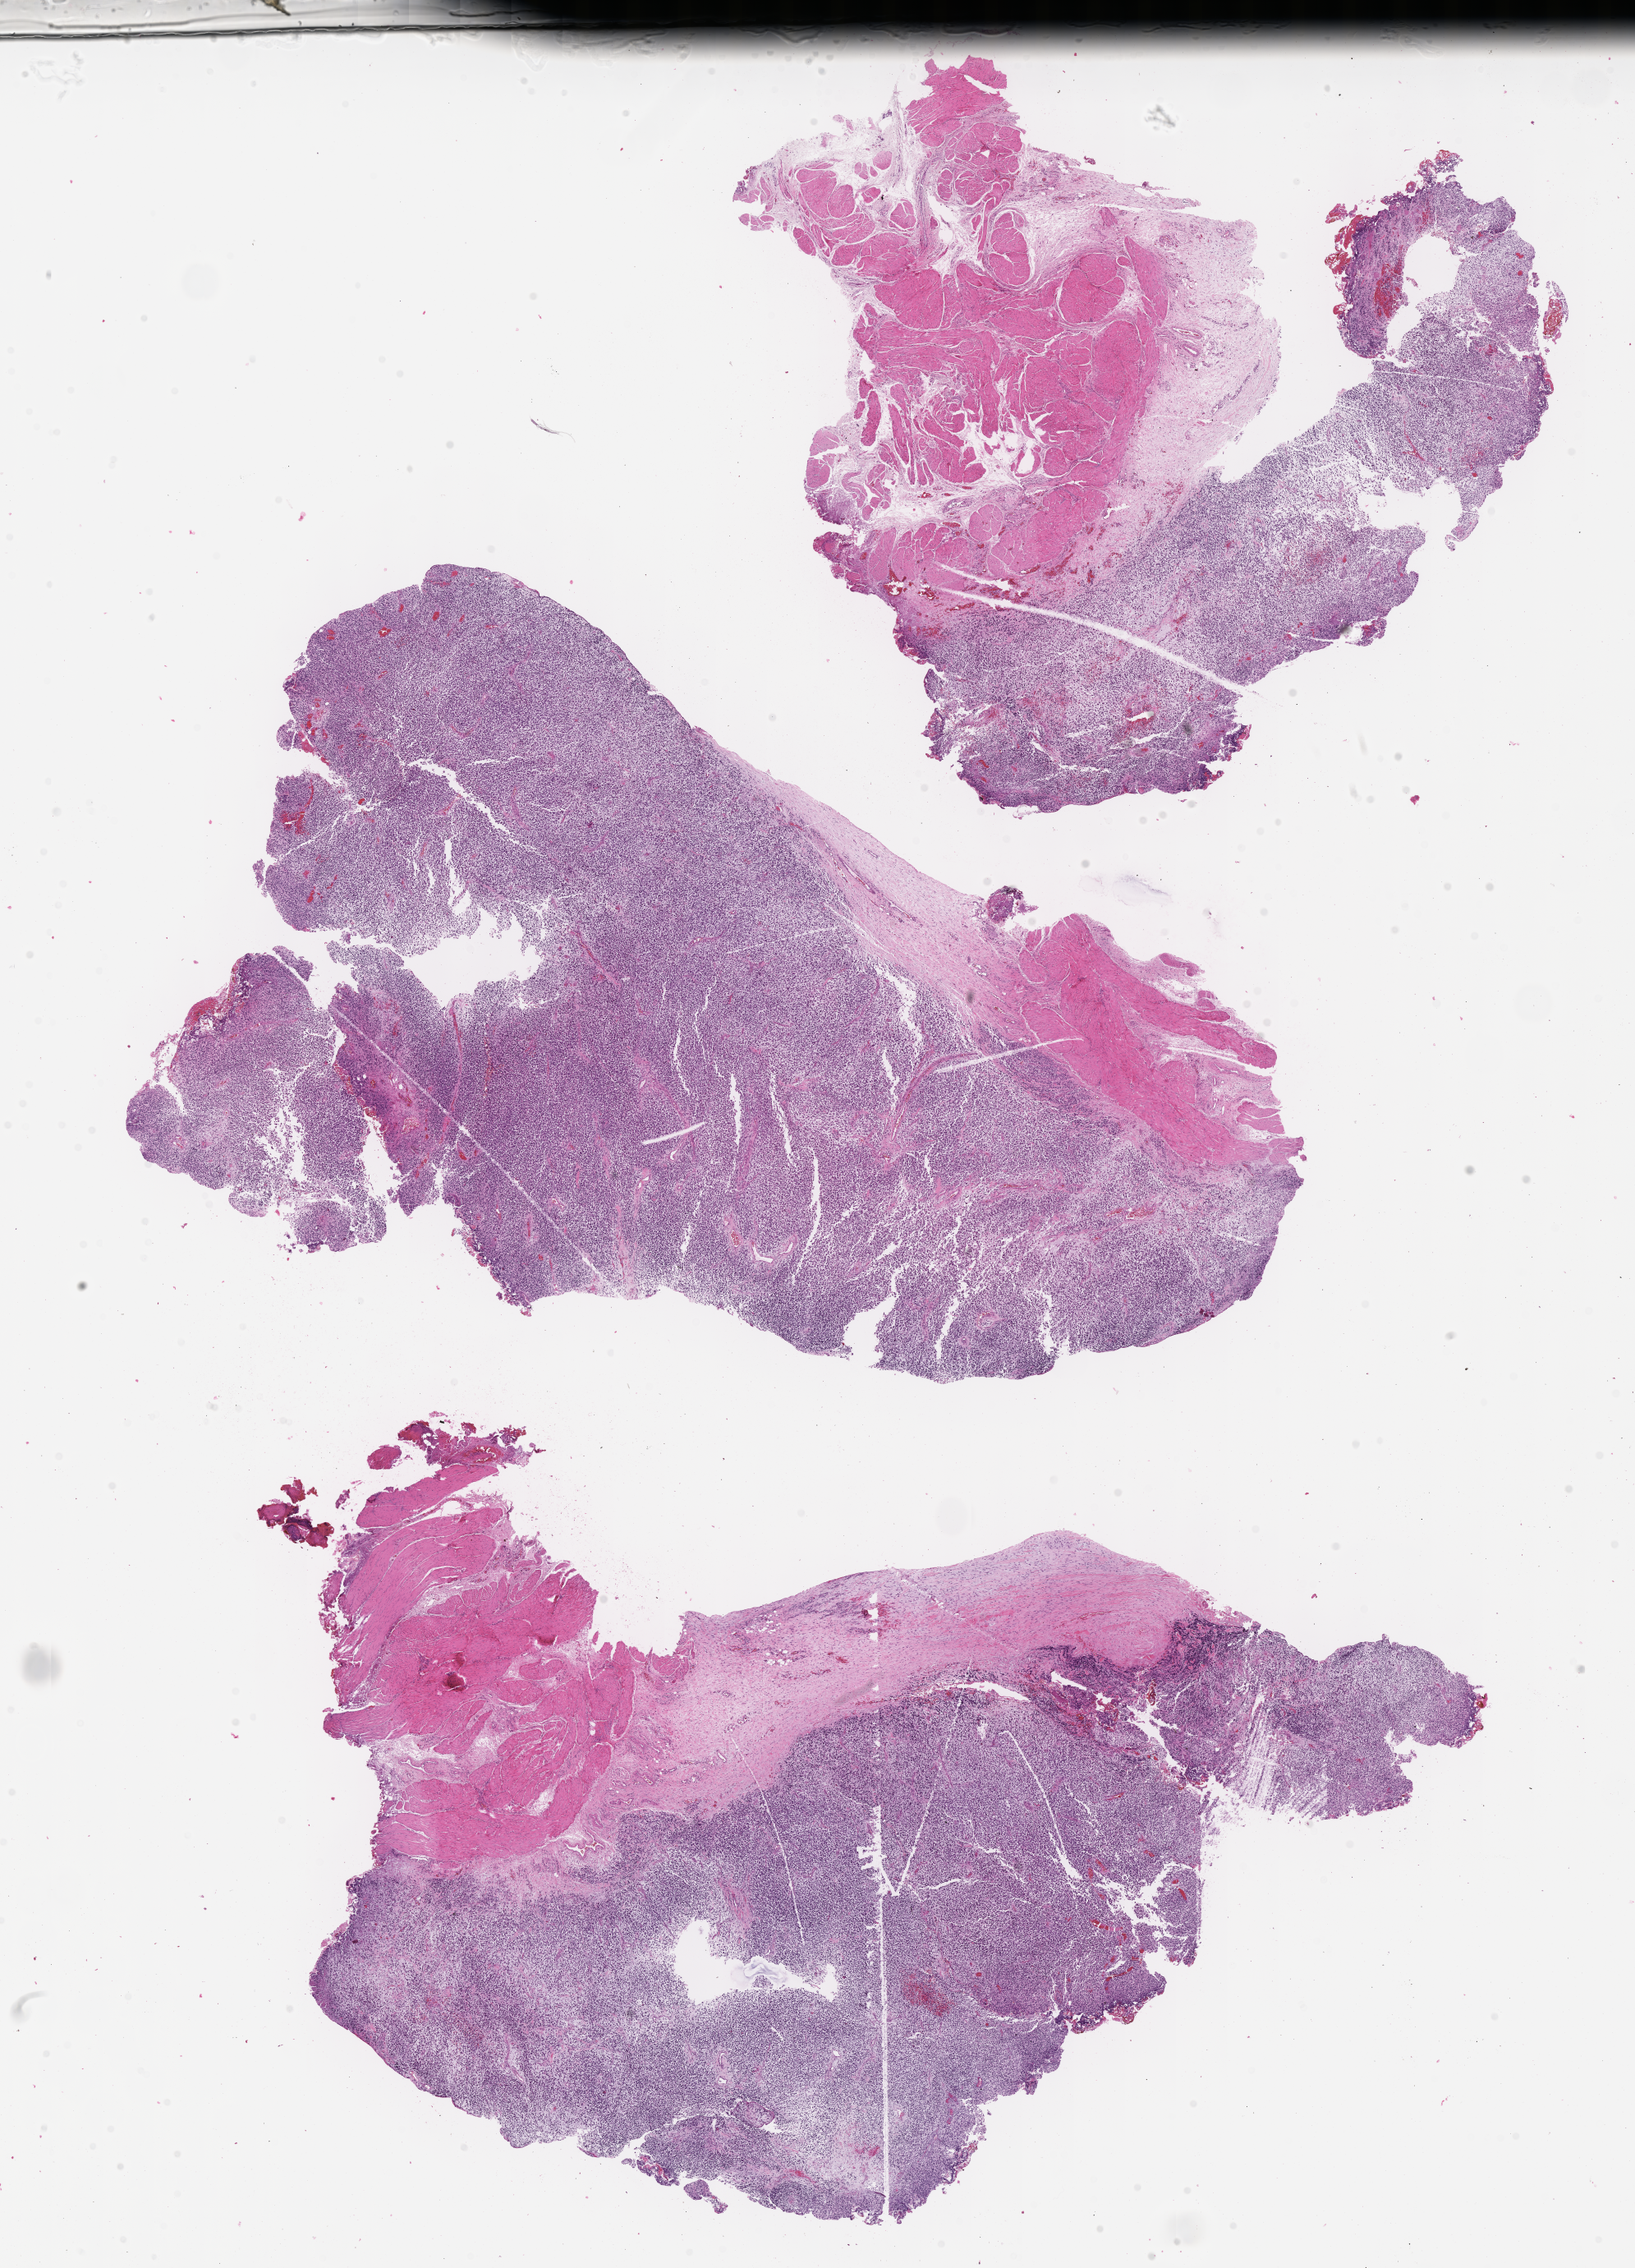
Digitized haematoxylin and eosin-stained section of tumor tissue, whole scanned area (about 16.1 x 22.3 mm) shown as a low-resolution overview; FFPE section; site: soft tissue, abdomen. Patient: male, age 6.2 years at diagnosis.
• primary site (case record): bladder
• metastatic status at presentation (as recorded): non-metastatic (unconfirmed)
• diagnosis: rhabdomyosarcoma; histological classification: embryonal rhabdomyosarcoma
• stage (as recorded): 3